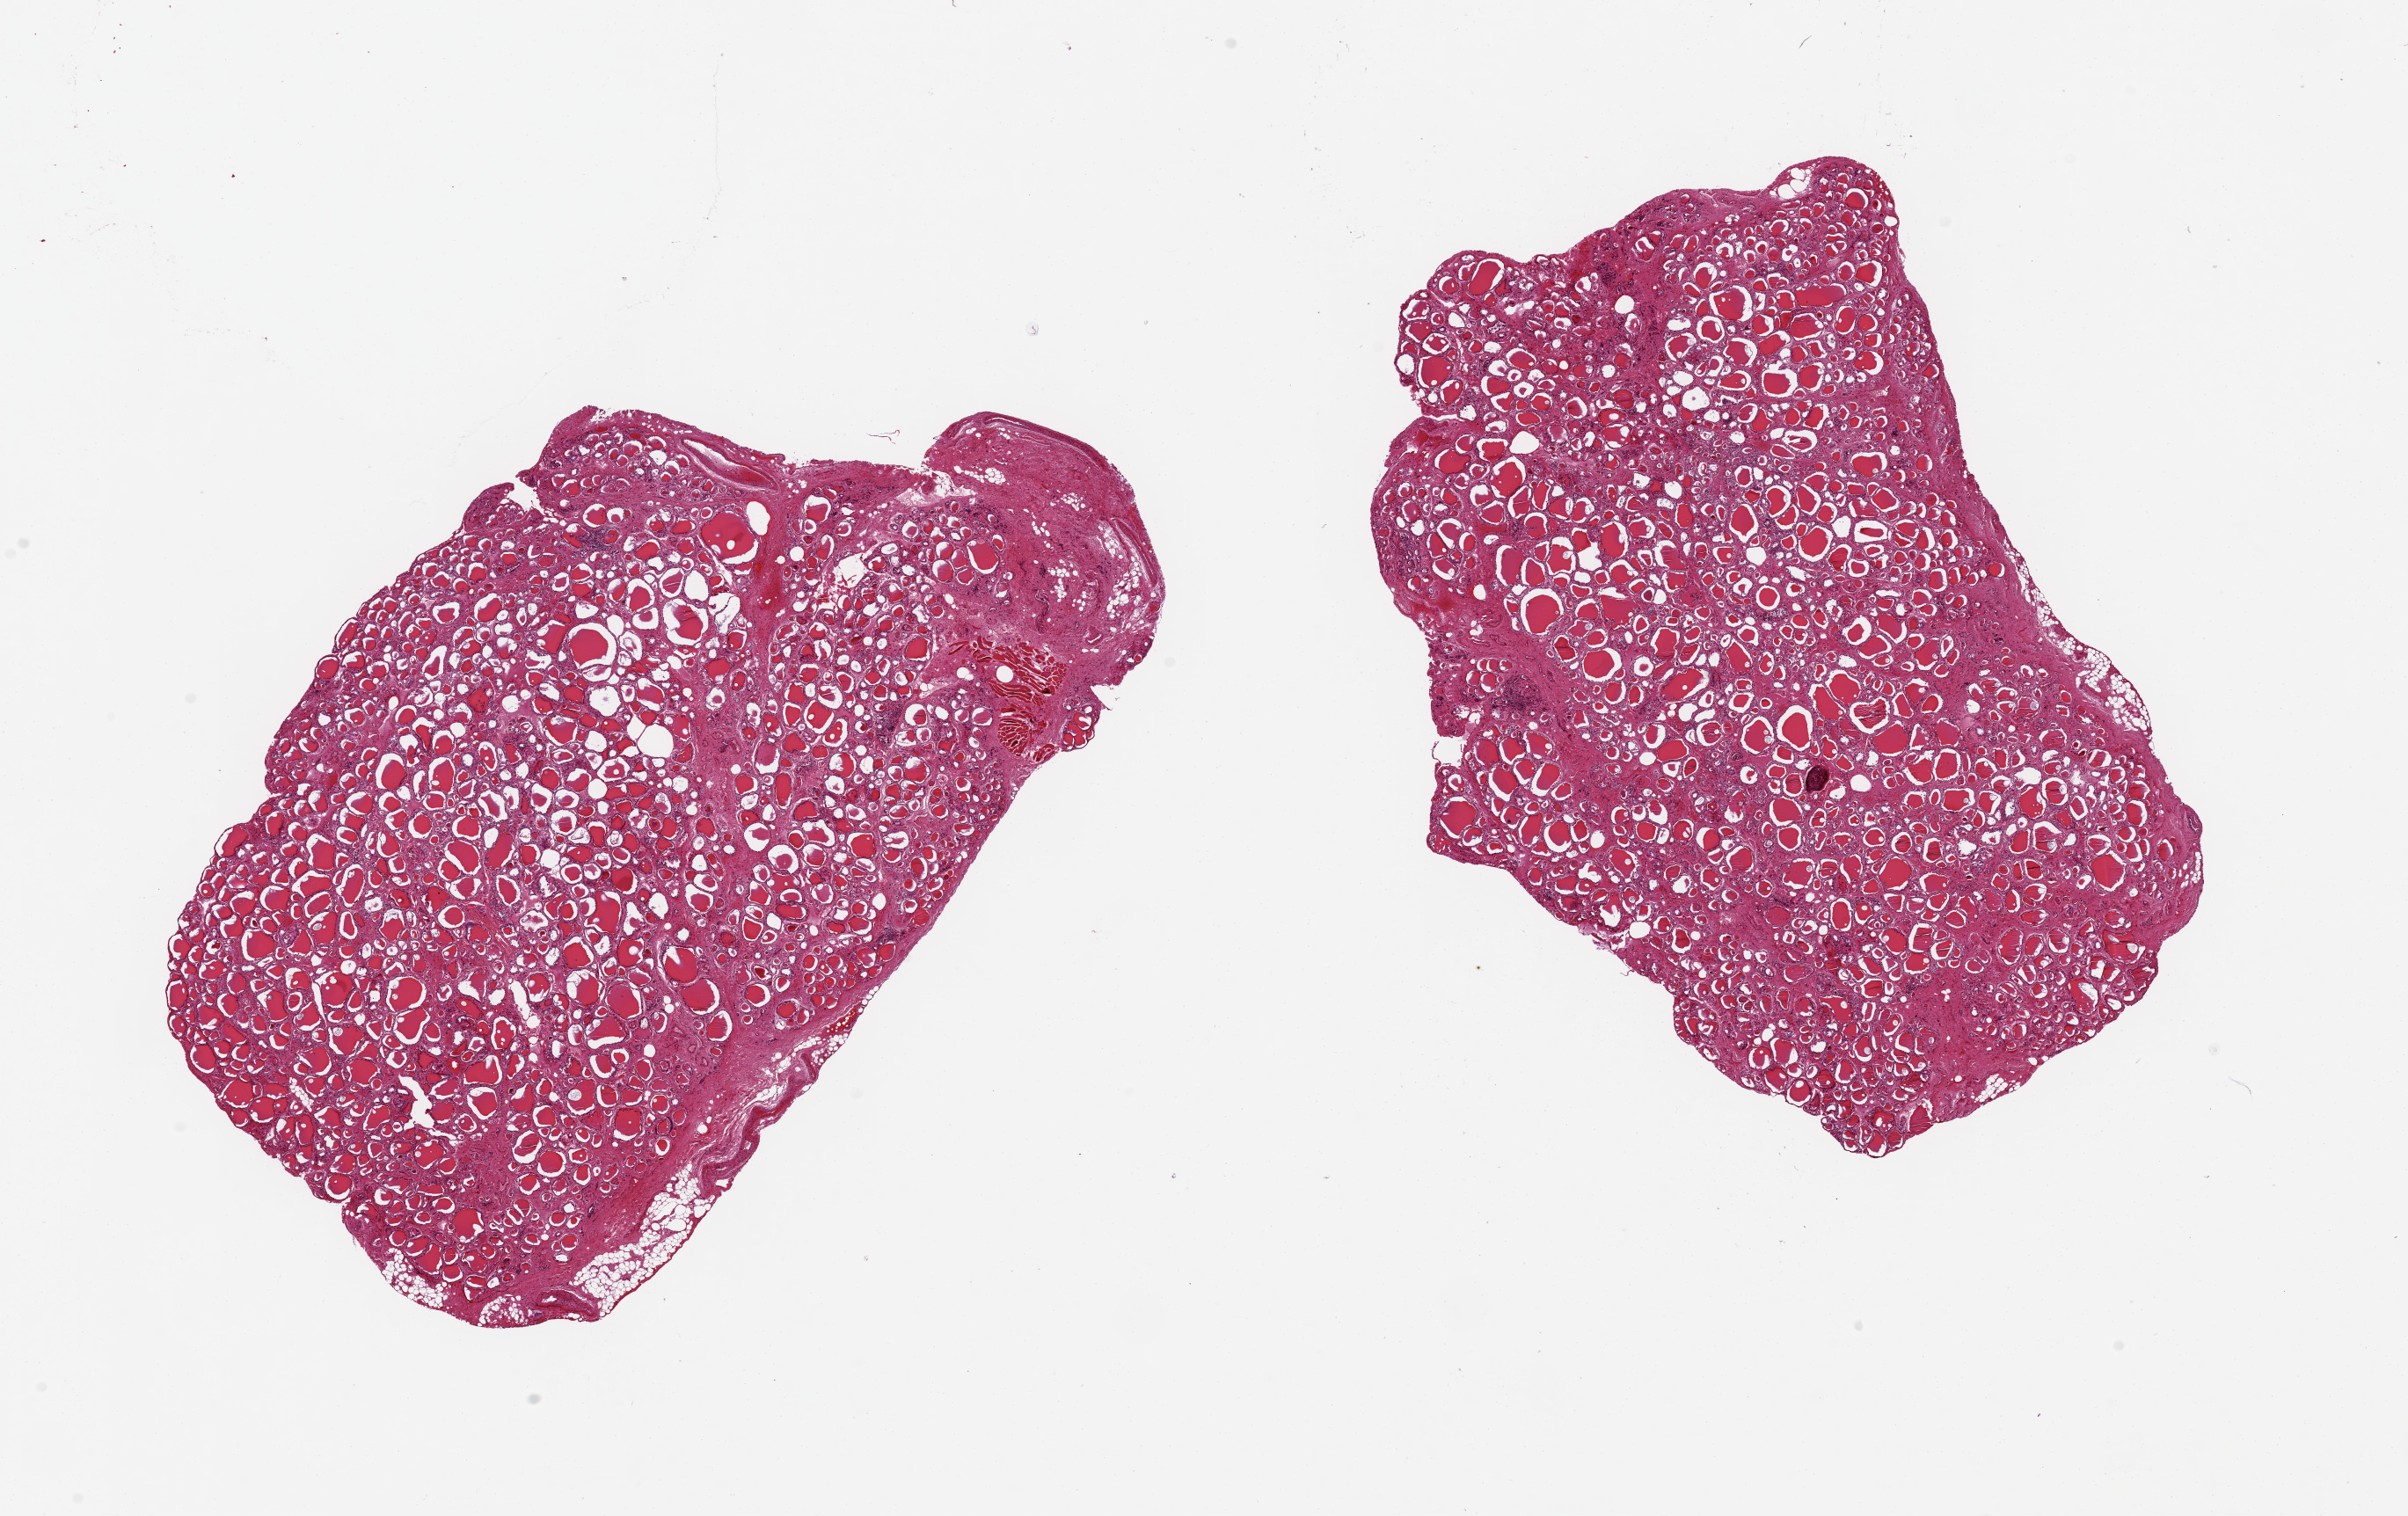
Digitized H&E-stained section, brightfield, a low-resolution overview of the entire scanned area, about 21.7 x 13.6 mm (slide scanned at 20x); PAXgene-fixed paraffin-embedded (PFPE) section; target tissue: thyroid; tissue donor sample. Male donor.
Pathologist's review note for this sample: 2 pieces ~8x5mm, good clean specimens.